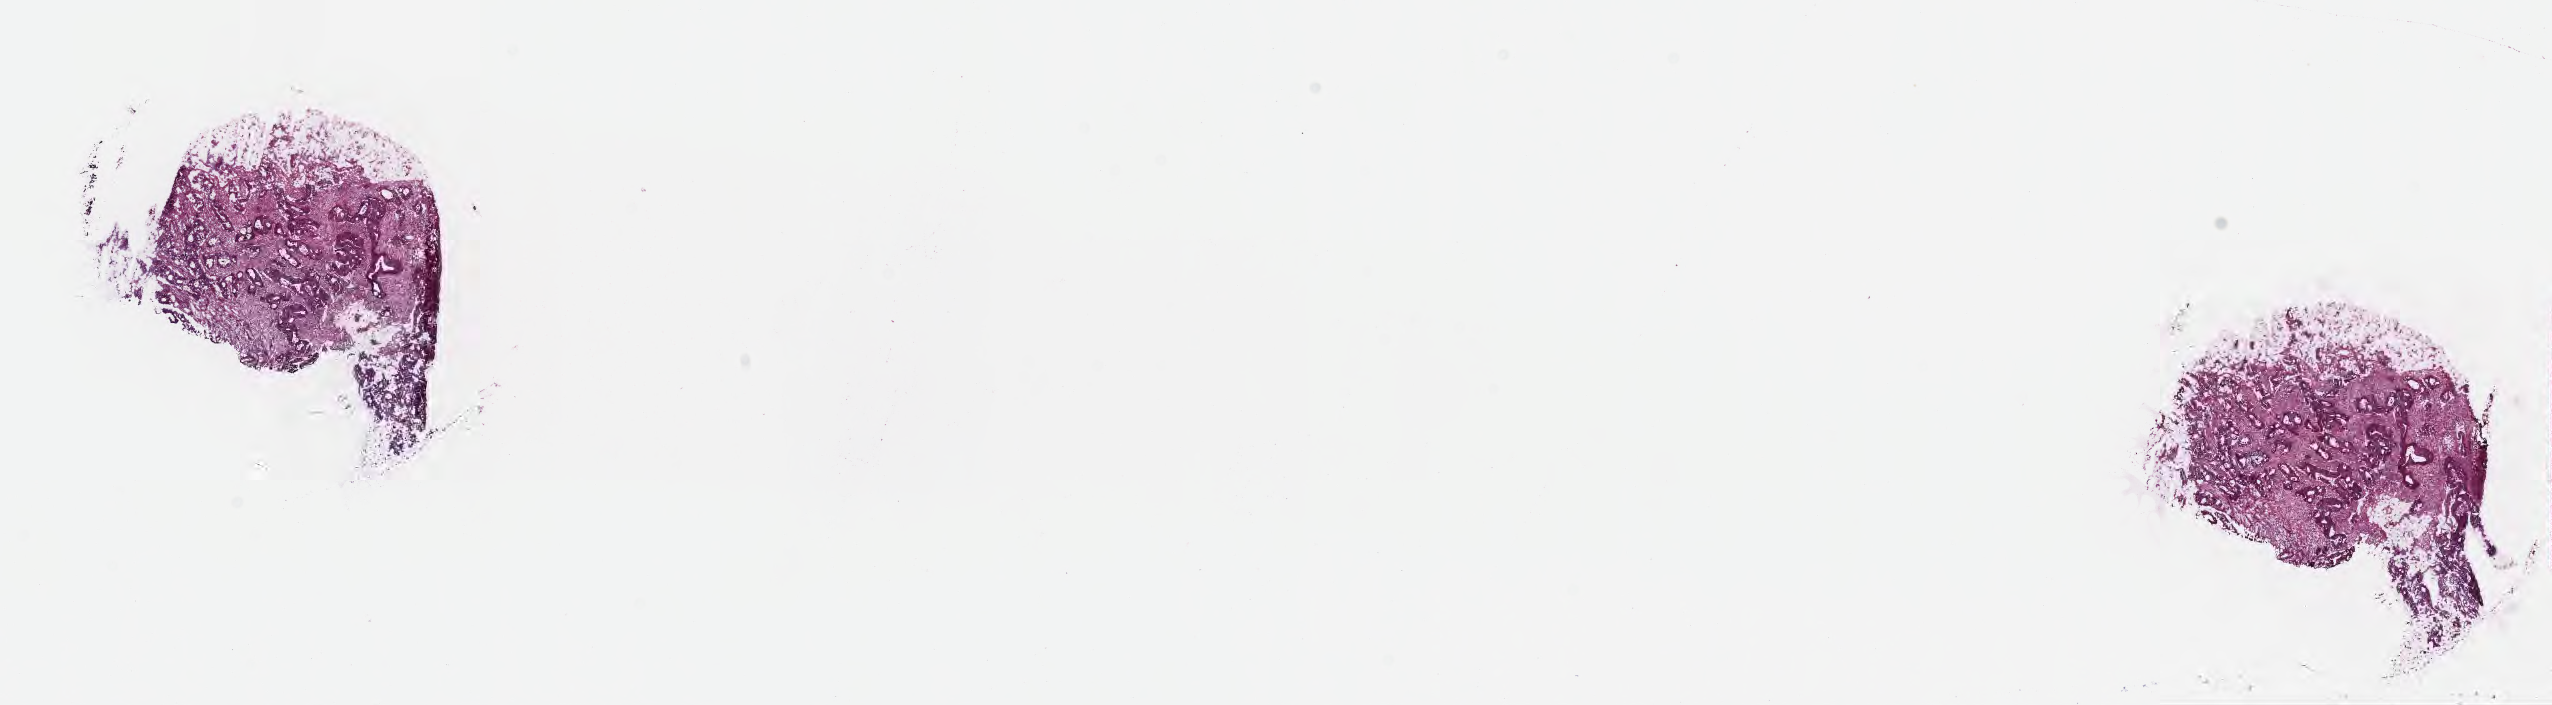
Digitized haematoxylin and eosin-stained section, a low-resolution overview of the entire scanned area, about 20.6 x 5.7 mm. Frozen section. Specimen: primary tumor. Site: sigmoid colon. Male patient; age at initial diagnosis 51 years. Tumor grade: G2 (moderately differentiated). Composition of this section per pathologist review: tumor cells 80%, tumor nuclei 80%, stromal cells 20%, necrosis 0%, normal cells 0%. Inflammatory infiltration, as recorded: lymphocyte infiltration 4%, monocyte infiltration 3%, neutrophil infiltration 7%.
- diagnosis: Adenocarcinoma, NOS
- section: bottom of the tissue portion
- AJCC pathologic stage: Stage IIIA